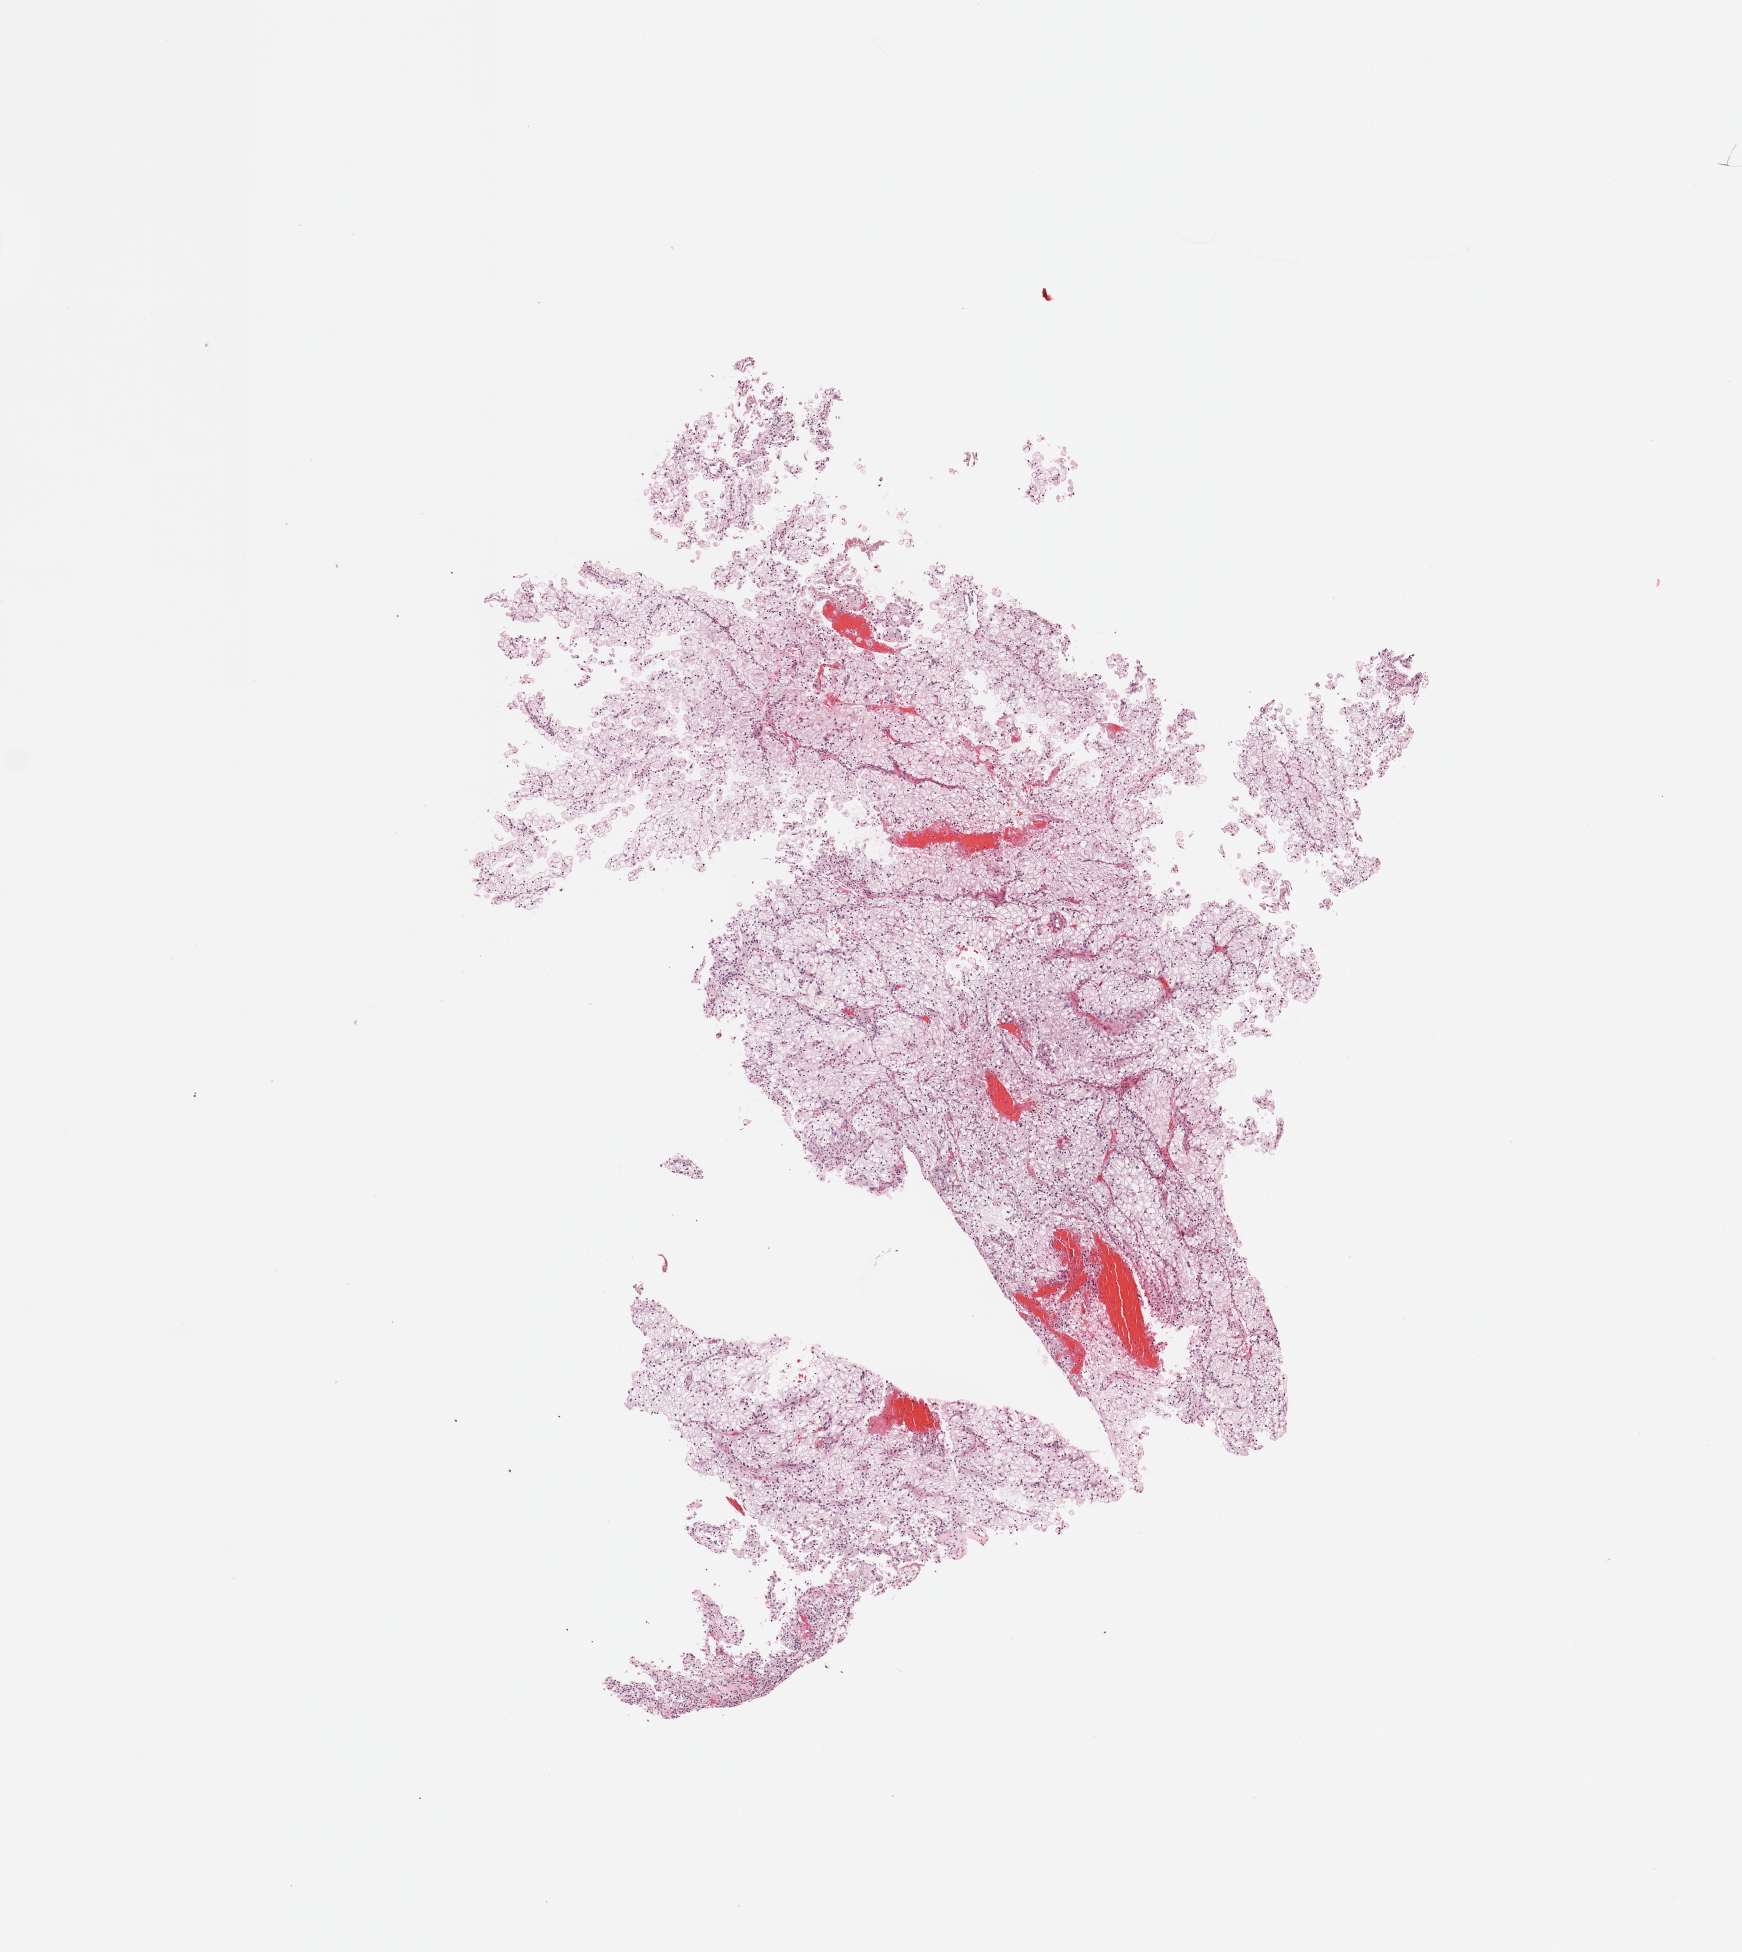
Digitized H&E tissue section (whole slide), a low-resolution overview of the entire scanned area, about 6.9 x 7.7 mm; tumour tissue sample, sampled site: kidney. Patient: male, age 61 years. Histologic grade: G3 (poorly differentiated). Pathologist review of this section (percent, as recorded): tumour nuclei 90%, necrosis 0%.
Primary tumour site (as recorded): upper pole. Histologic diagnosis: Renal cell carcinoma, NOS. AJCC pathologic stage: III.